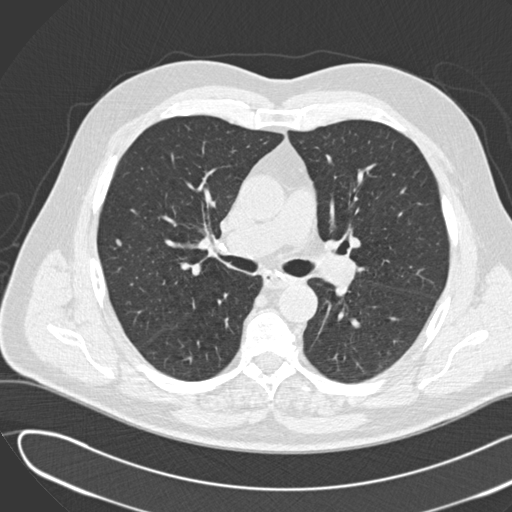
Low-dose screening chest CT, one axial slice. Position 84 of 155 along the scan axis. Reconstruction kernel B30f. Lung window (W 1500 / L -600 HU). 2 mm slice thickness. 512 × 512 image matrix.
Structures marked on this image (outlined manually by an expert reader):
- lesion 1 (tumor, lower lobe of right lung): bounding box [x1, y1, x2, y2] px = [115, 239, 122, 246]